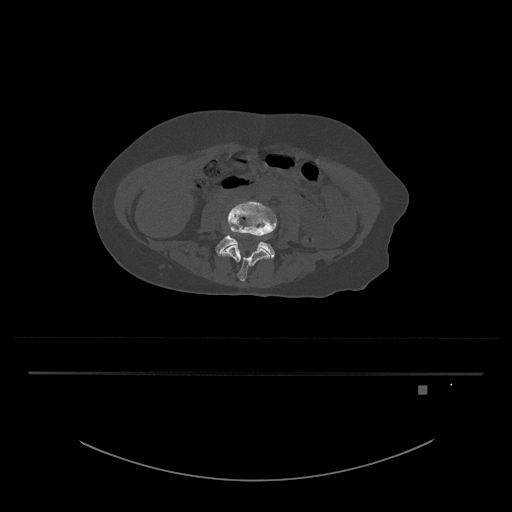
CT including the spine, one axial slice; slice 338 of 797 in the series (ordered by position); bone window (W 1800 / L 400 HU); 0.5 mm slice thickness; 512 × 512 image matrix, field of view 500 × 500 mm. Patient: female, 57 years. From the clinical record (not read from this slice): primary cancer: cervical.
Annotated regions visible in this slice (semi-automatic segmentation, software-assisted and operator-edited):
- L4 vertebra: bounding box (x1, y1, x2, y2) in pixels: (220, 201, 277, 281)